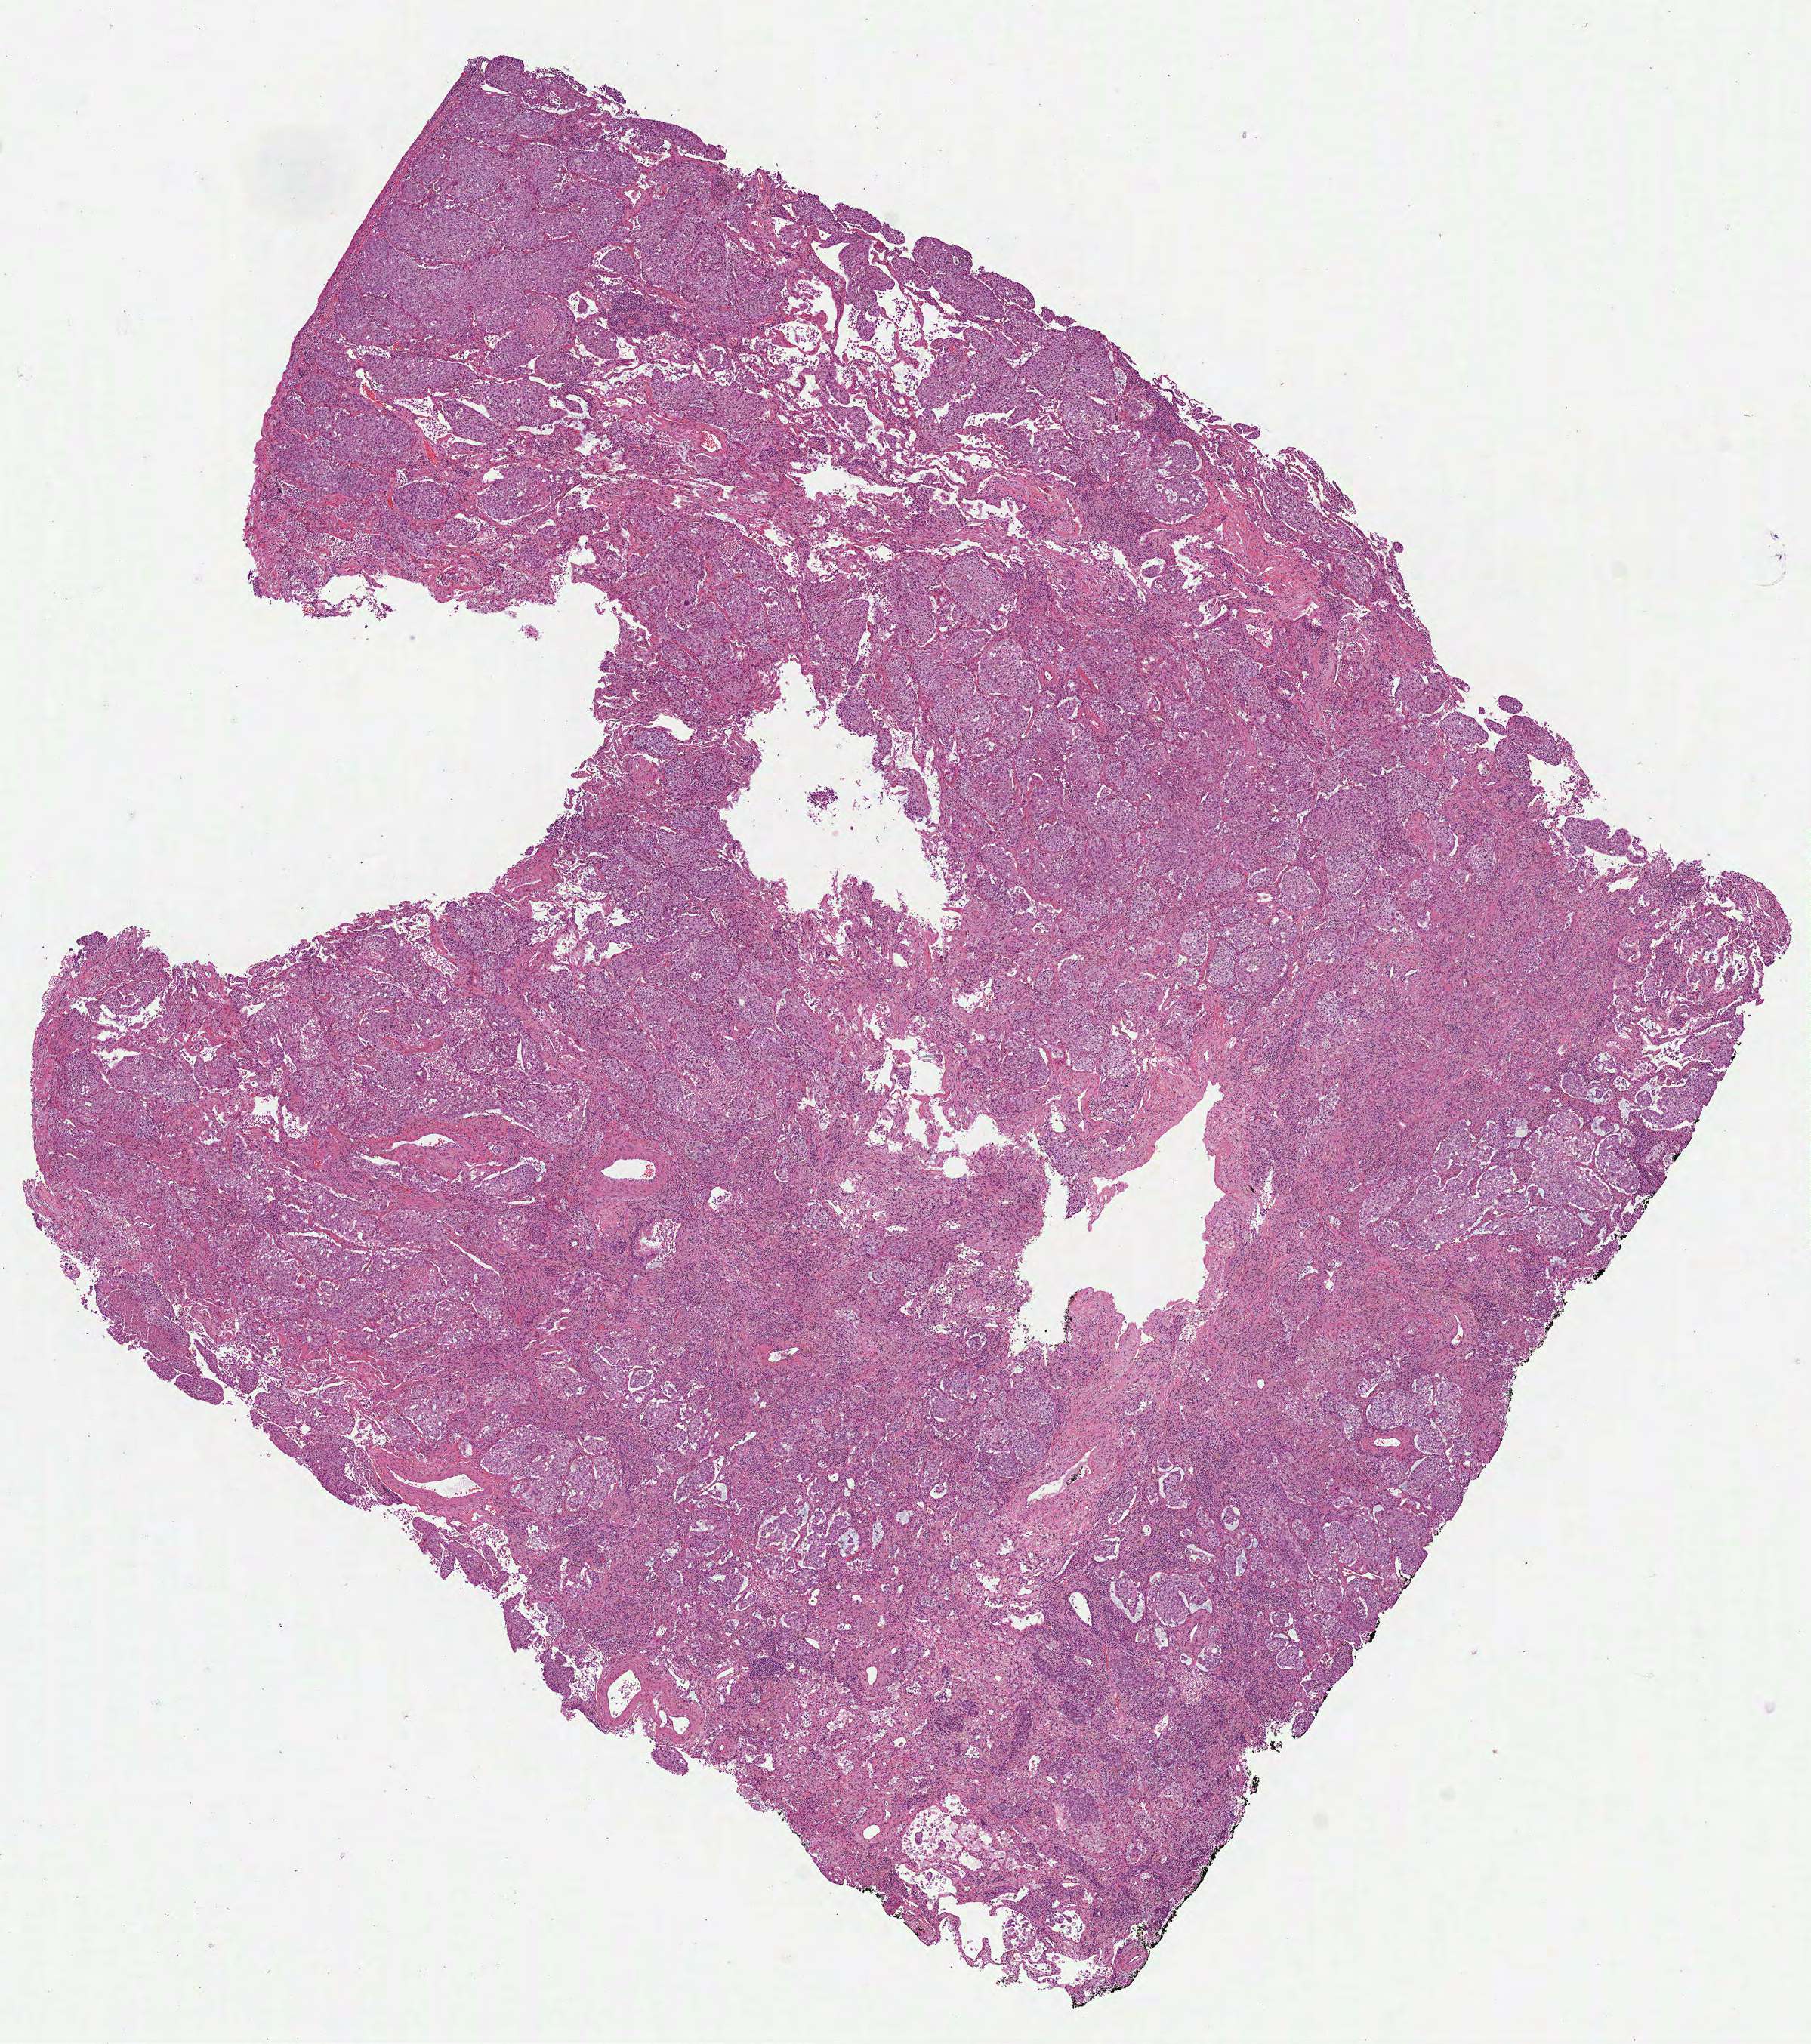
Whole-slide histology image, Hematoxylin and eosin (H&E) stained, shown as a low-resolution overview of the whole scanned area (about 9.7 x 10.9 mm, from a 40x scan), formalin-fixed paraffin-embedded (FFPE) diagnostic section, sample: primary tumour, lung. Female patient; age at initial diagnosis 66 years.
* histologic diagnosis: Squamous cell carcinoma, NOS (lower lobe, lung)
* AJCC pathologic stage: IIIA (7th edition)